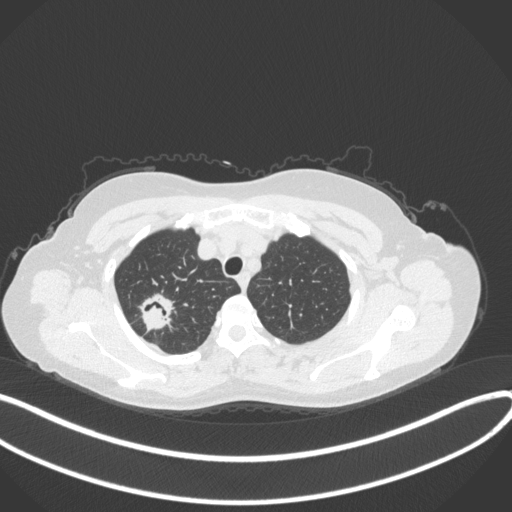
Chest CT, one axial slice; position 303 of 342 along the scan axis; lung window (W 1500 / L -600 HU); 1 mm slice thickness; 512 × 512 image matrix. Patient: female, 50 years. From the clinical record (not read from this slice): clinical TNM (as recorded): T1c N0 M0; histopathological grade: G2-3.
Structures marked on this image (bounding box drawn by a radiologist):
- lung tumour (recorded histology: adenocarcinoma): bounding box [x1, y1, x2, y2] px = [136, 291, 178, 329]